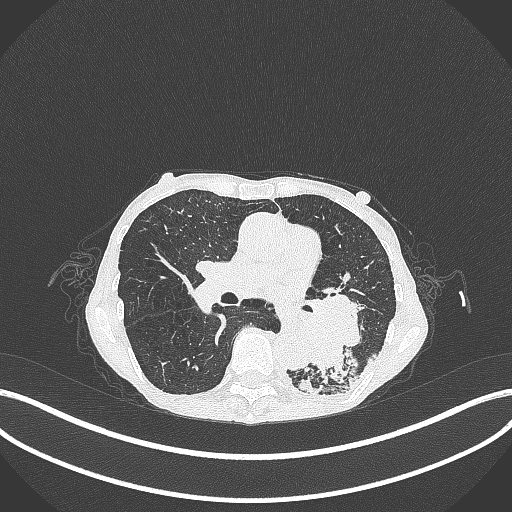
Chest CT, one axial slice; slice 143 of 347 in the series (ordered by position); lung window (W 1500 / L -600 HU); 1 mm slice thickness; 512 × 512 image matrix, field of view 400 × 400 mm. Patient: female, 70 years. From the clinical record (not read from this slice): clinical TNM (as recorded): T3 N0 M0; histopathological grade: G3.
Structures marked on this image (bounding box drawn by a radiologist):
- lung tumour (recorded histology: small cell carcinoma): bounding box [x1, y1, x2, y2] px = [290, 284, 369, 389]